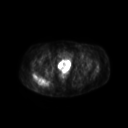
FDG PET of an extremity soft-tissue mass (from a PET/CT study), one axial slice; position 48 of 267 along the scan axis; 128 × 128 image matrix, field of view 600 × 600 mm. Female patient, age 60 years. From the clinical record (not read from this slice): histological type: spindle cell suggestive of myxofibrosarcoma; grade: intermediate; site of the primary tumour: right buttock.
Annotated regions visible in this slice (expert contour drawn on MRI and transferred to this co-registered scan by the dataset authors):
- gross tumour volume (mass): box from (x=32, y=73) to (x=49, y=86) px